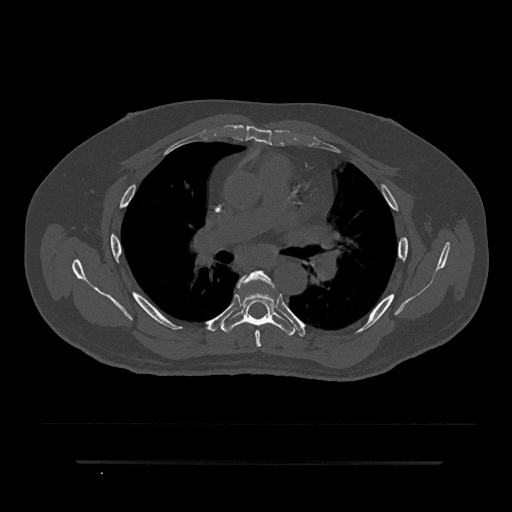
CT including the spine, one axial slice. Position 544 of 797 along the scan axis. Reconstruction kernel Br40s/3. Bone window (W 1800 / L 400 HU). 0.5 mm slice thickness. 512 × 512 image matrix, field of view 464 × 464 mm. Patient: male, 59 years. Case-level facts recorded for this patient, not image findings: primary cancer: bile ducts.
Outlined on this slice (semi-automatic segmentation, software-assisted and operator-edited):
- T5 vertebra: box from (x=237, y=271) to (x=275, y=347) px
- T6 vertebra: (x=221, y=284)–(x=294, y=336)